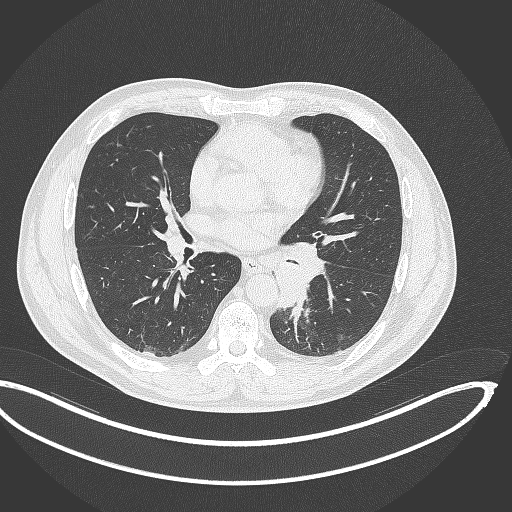
Chest CT, one axial slice. Slice 177 of 362 in the series (ordered by position). Reconstruction kernel B70f. Lung window (W 1500 / L -600 HU). 1 mm slice thickness. 512 × 512 image matrix, field of view 442 × 442 mm. Patient: male, 50 years. From the clinical record (not read from this slice): clinical TNM (as recorded): T2a N3 M0.
Structures marked on this image (rectangle marked by the reading radiologist):
- lung tumour (recorded histology: squamous cell carcinoma): bounding box (x1, y1, x2, y2) in pixels: (272, 237, 325, 312)